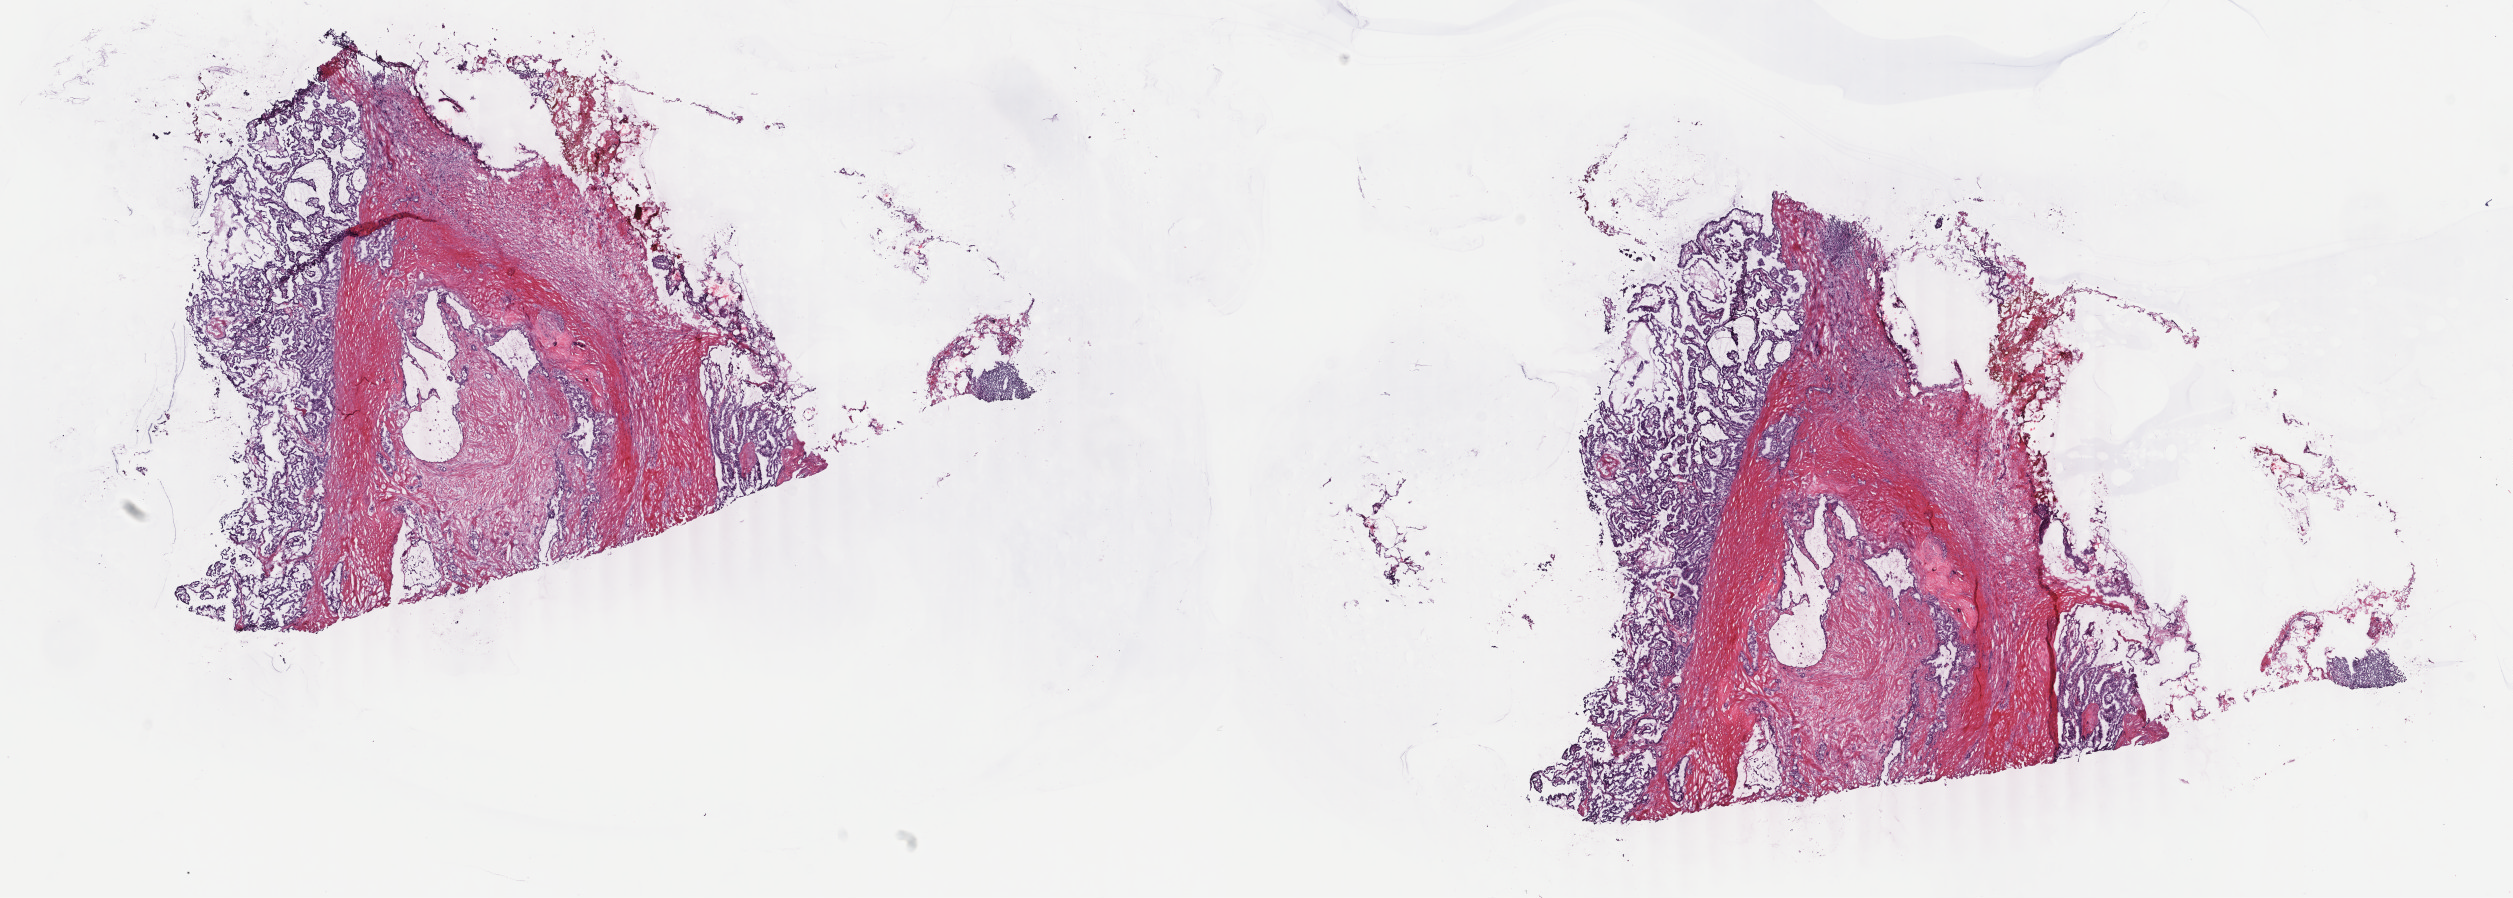
H&E whole-slide image, whole scanned area (about 20.0 x 7.1 mm, acquisition: 40x scan) shown as a low-resolution overview. Frozen section from the top of the tissue portion. Sample: primary tumour, thyroid. Patient: male, age at initial diagnosis 64 years. Pathologist review of this section (percent, as recorded): tumour cells 70%, tumour nuclei 65%, normal cells 0%, stromal cells 30%, necrosis 0%. Infiltration values recorded for this section: lymphocyte infiltration 0%, monocyte infiltration 0%, neutrophil infiltration 0%.
- laterality: right
- histologic diagnosis: Papillary adenocarcinoma, NOS (thyroid gland)
- AJCC pathologic stage: IVA (7th edition)
- lymph nodes positive (case pathology): 14 of 28 examined